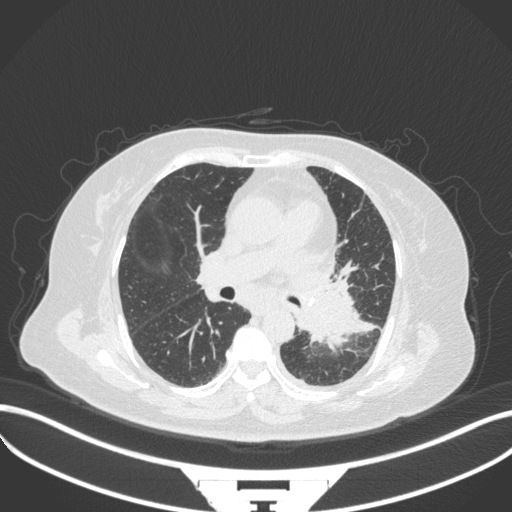
Chest CT, one axial slice. Position 193 of 328 along the scan axis. Reconstruction kernel B31f. 120 kVp. Lung window (W 1500 / L -600 HU). 1 mm slice thickness. 512 × 512 image matrix. Patient: female, 69 years. Case-level facts recorded for this patient, not image findings: clinical TNM (as recorded): T2b N3 M1.
Annotated regions visible in this slice (bounding box drawn by a radiologist):
- lung tumour (recorded histology: adenocarcinoma): box from (x=293, y=268) to (x=380, y=349) px